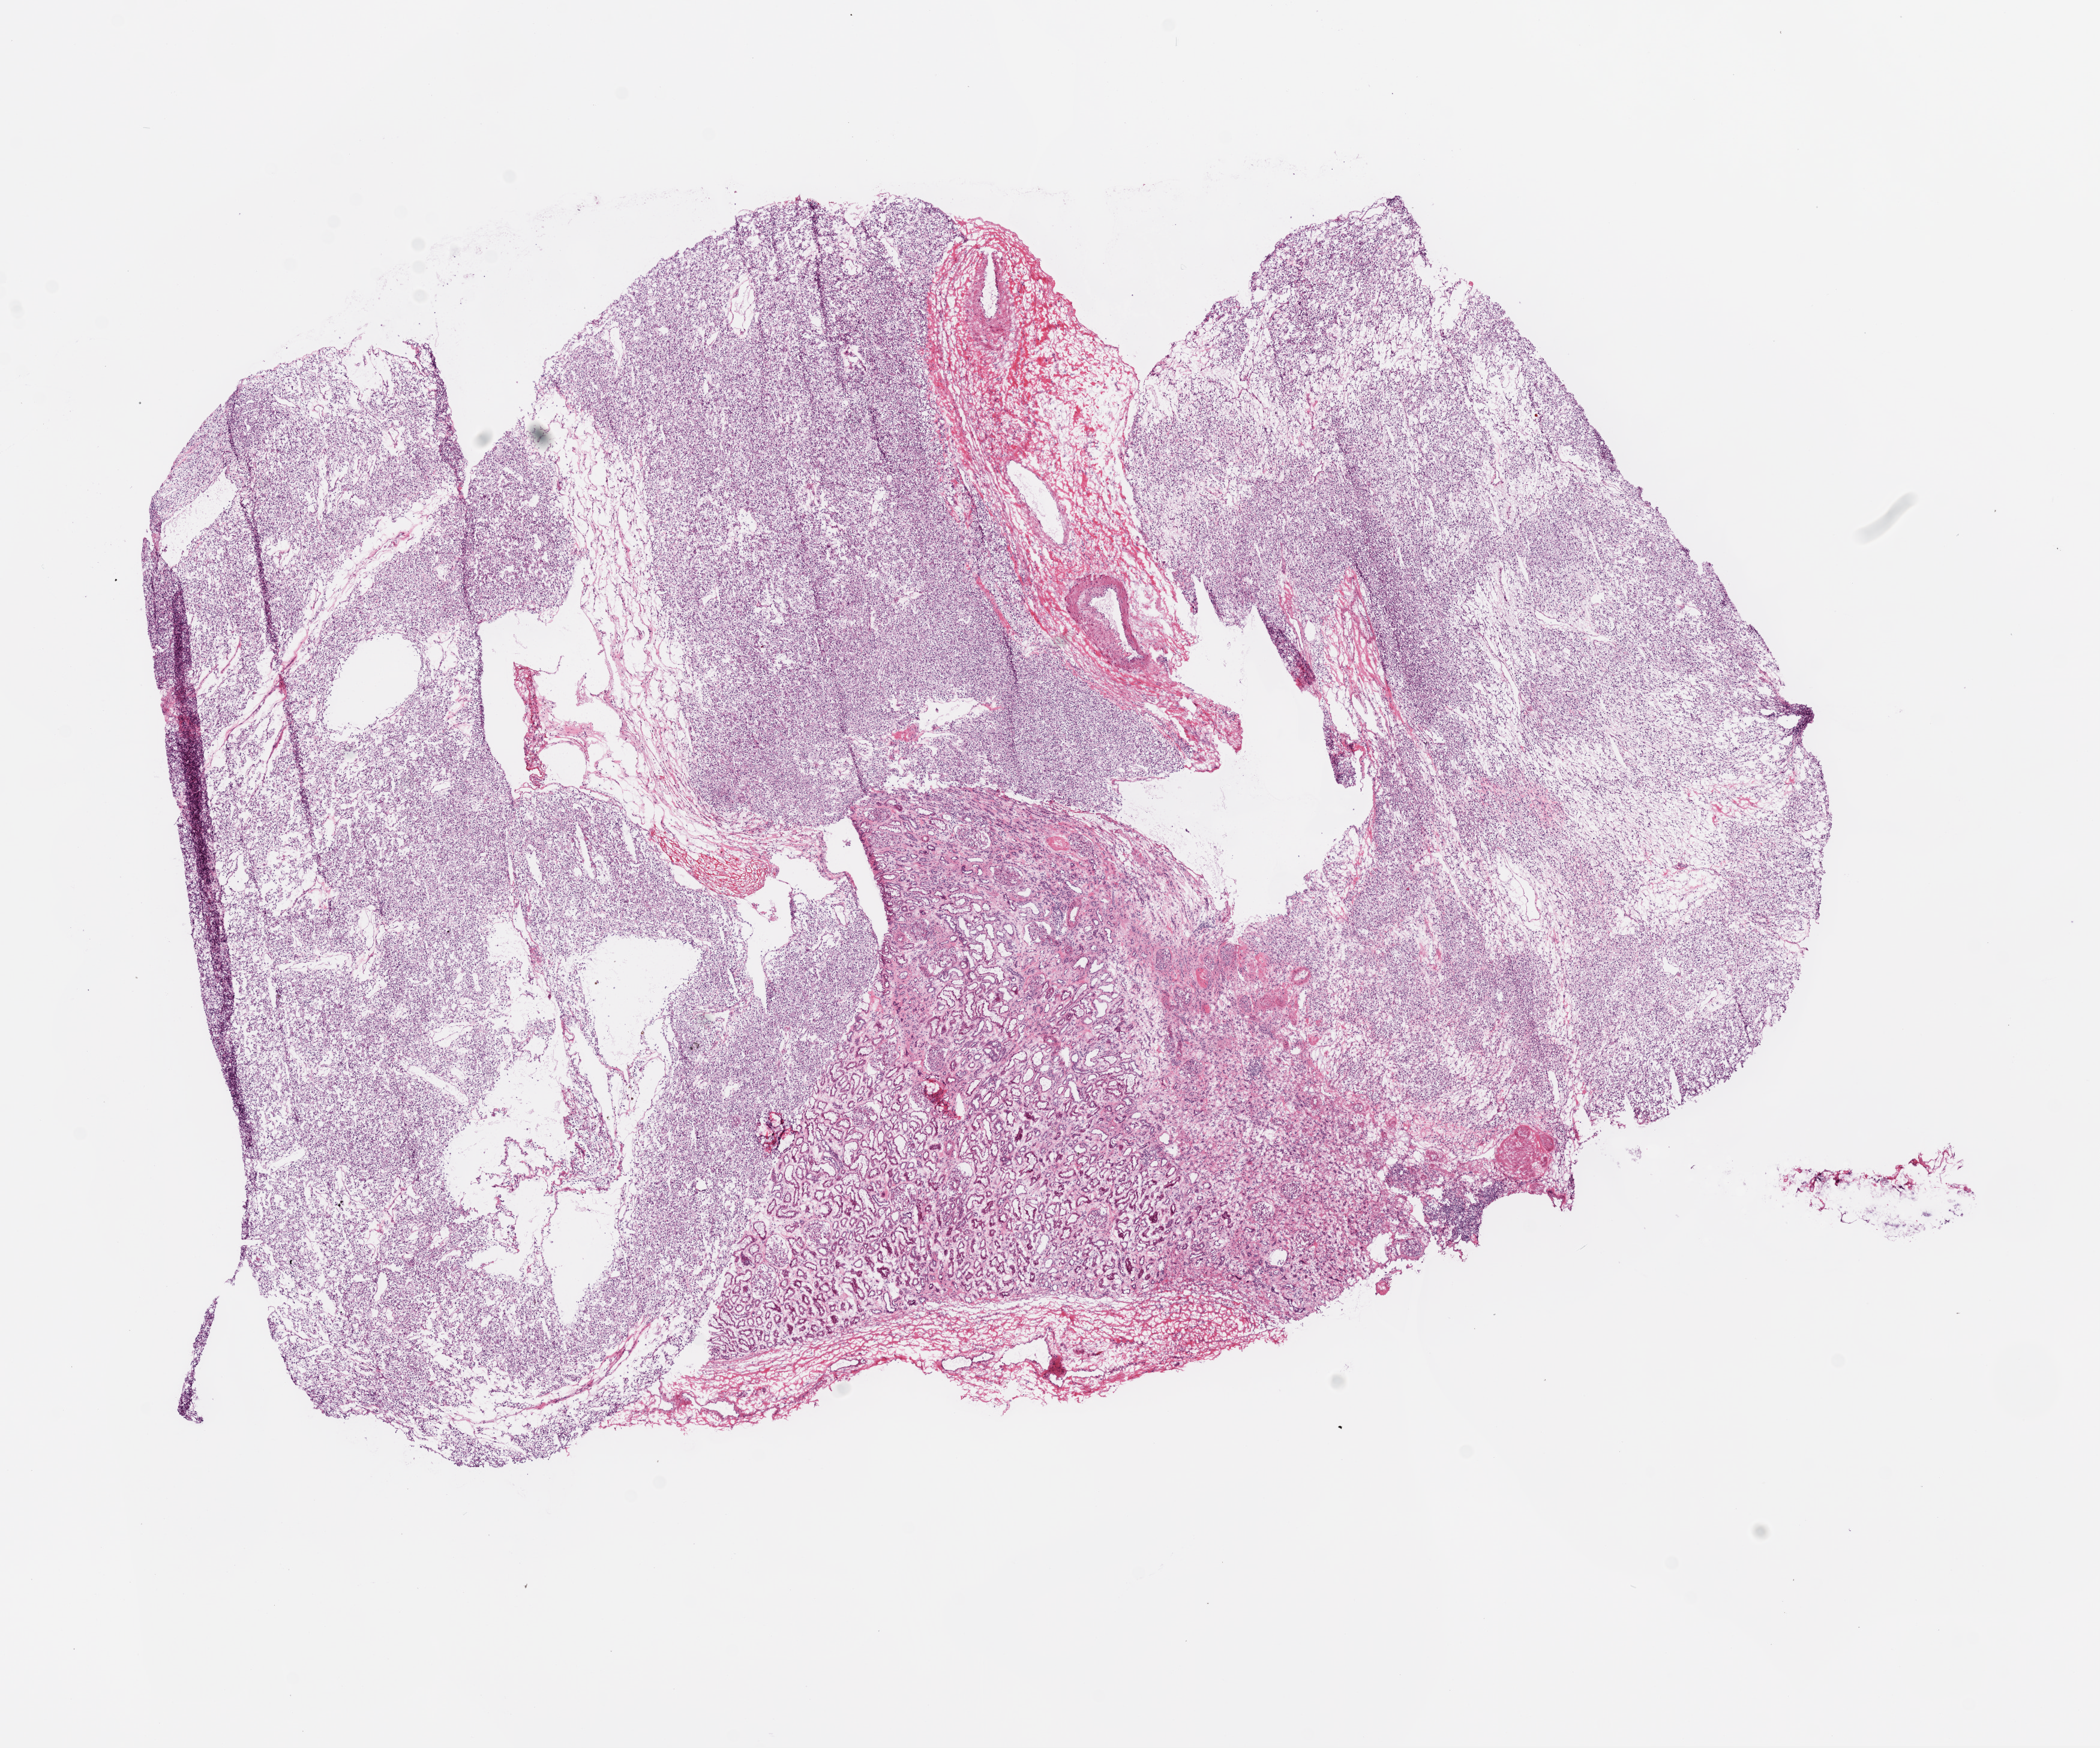
Whole-slide histology image, H&E-stained — shown as a low-resolution overview of the whole scanned area (about 14.0 x 11.7 mm, slide scanned at 20x). Frozen section. Primary tumour sample from the kidney. Patient: female, age at initial diagnosis 60 years. Histologic grade: G2 (moderately differentiated). Pathologist review of this section (percent, as recorded): tumour cells 70%, tumour nuclei 70%, normal cells 25%, stromal cells 5%, necrosis 0%.
• AJCC pathologic stage: I
• histologic diagnosis: Clear cell adenocarcinoma, NOS